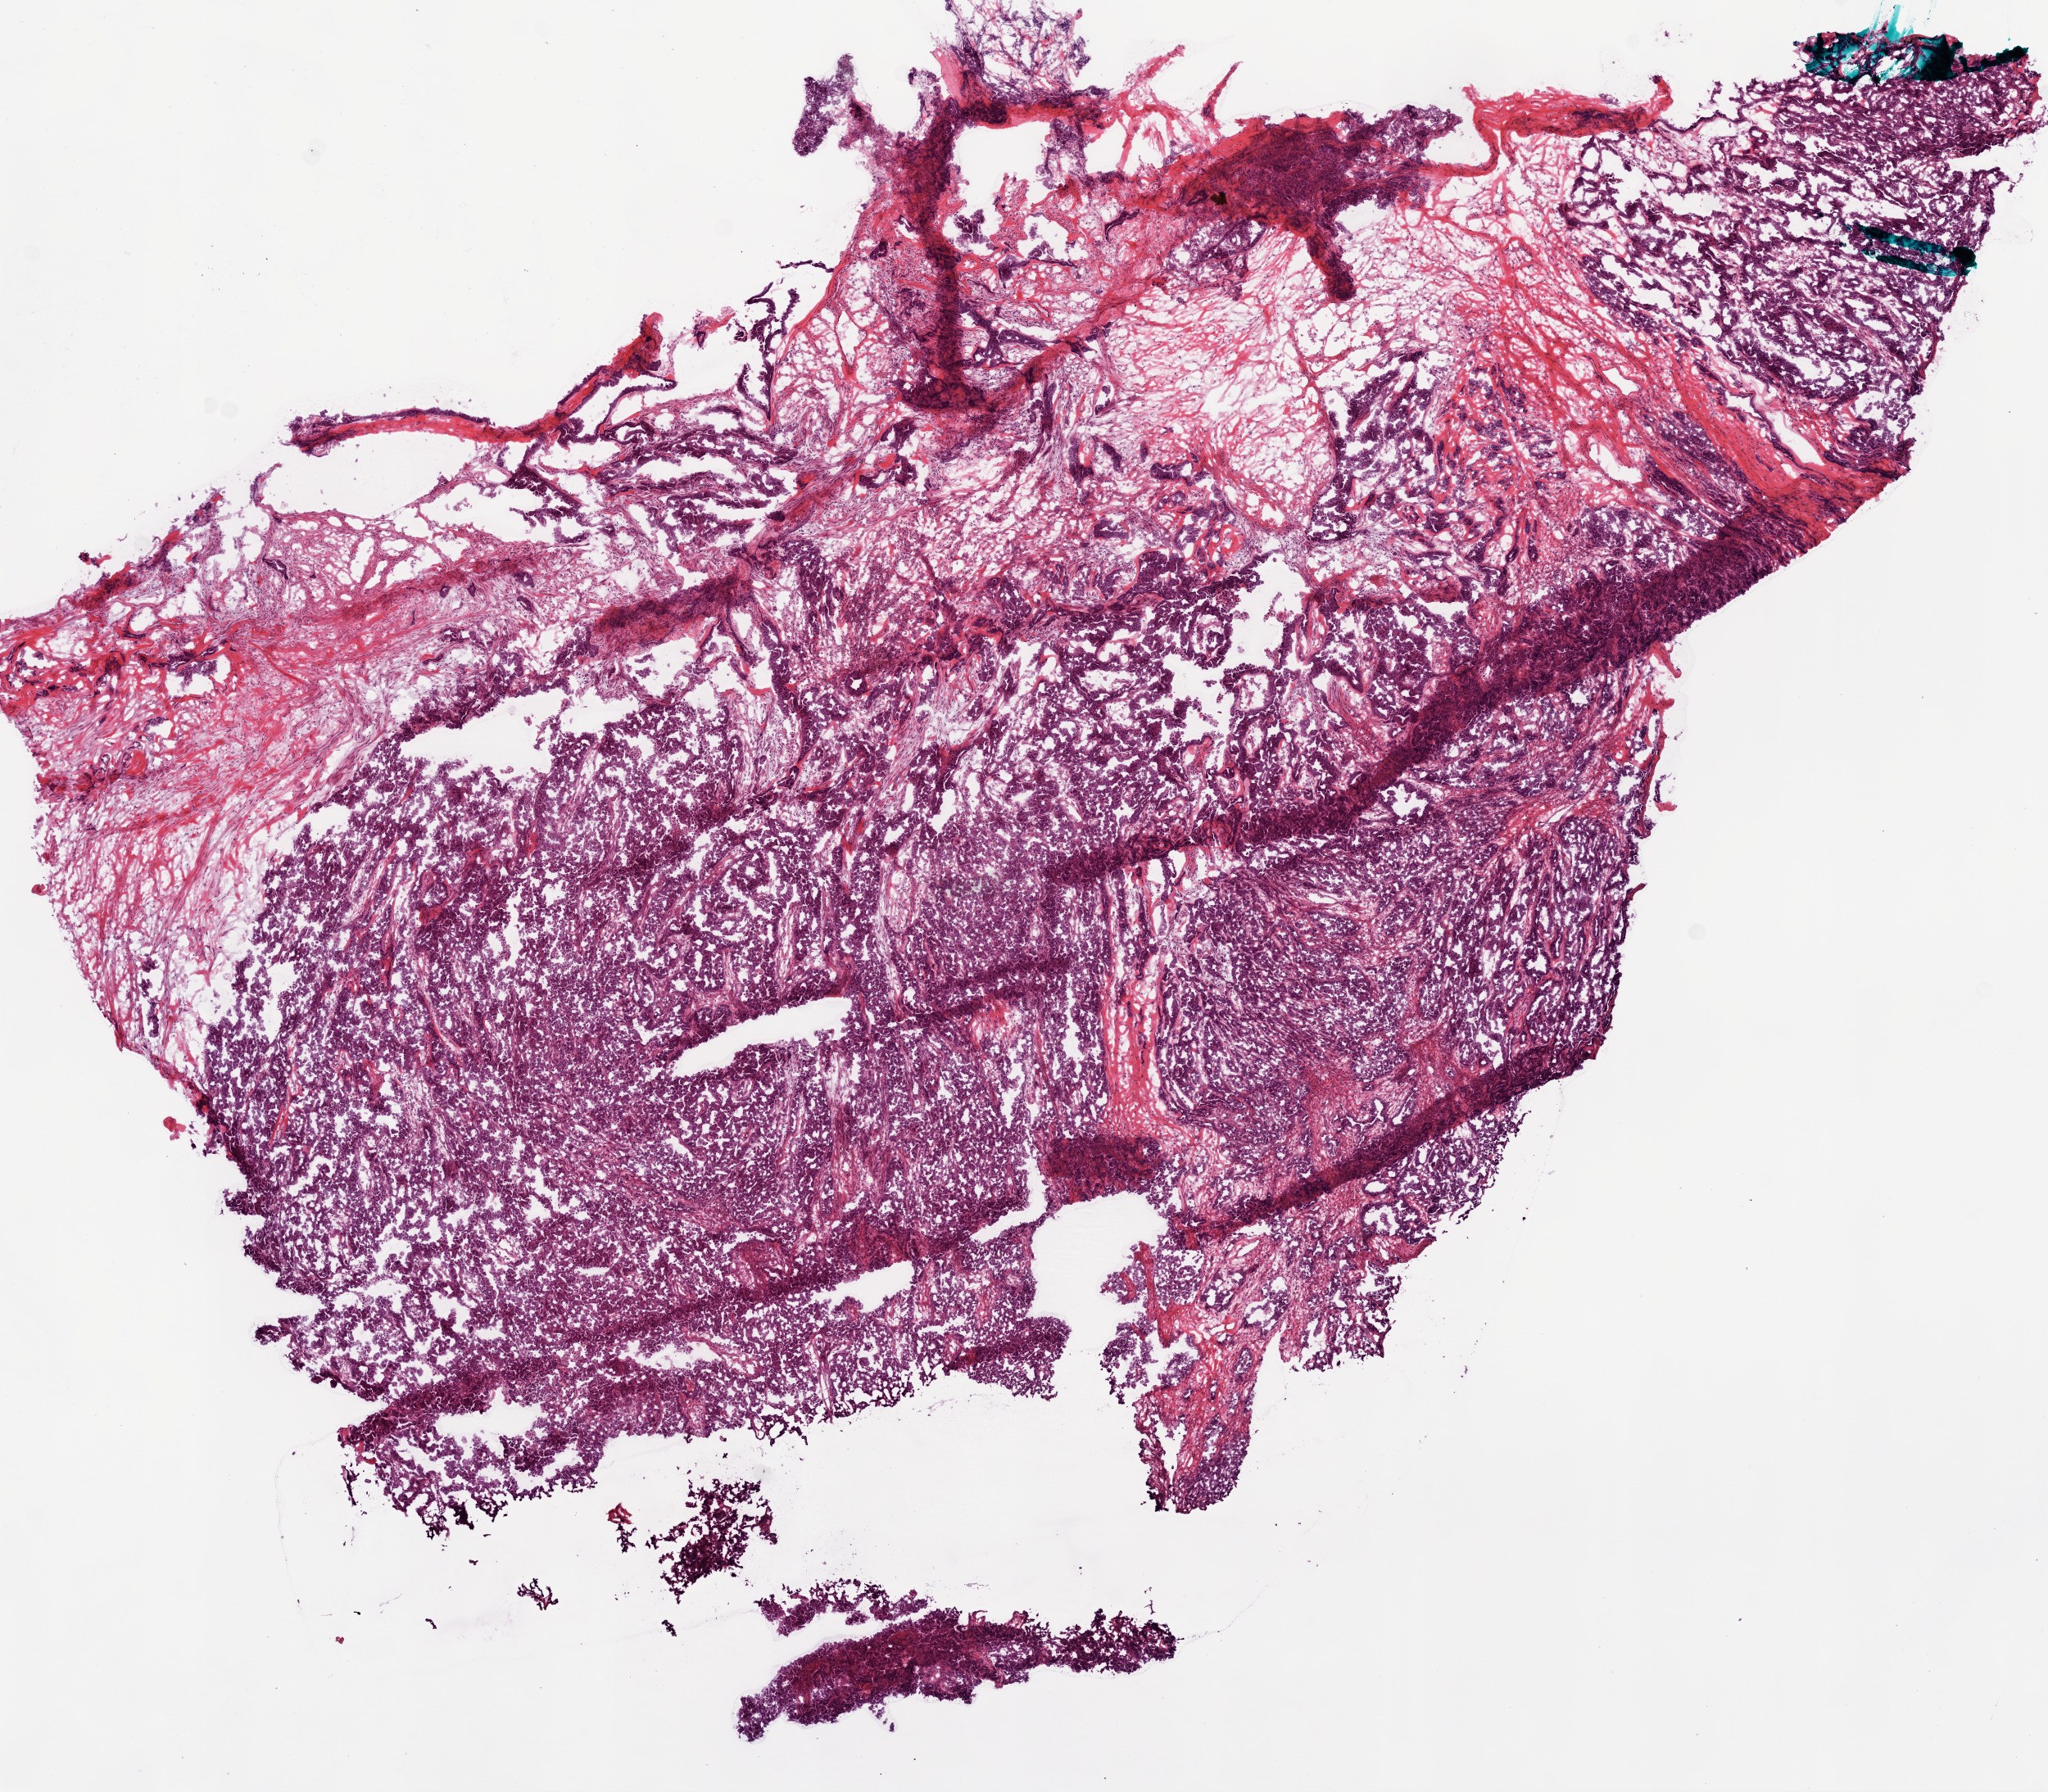
Whole-slide histology image, Hematoxylin and eosin (H&E) stained — low-resolution overview of the scanned area, about 10.0 x 8.8 mm (from a 20x scan); frozen section; ovary, primary tumour sample. Female, age 70 years at initial diagnosis. Histologic grade: G3 (poorly differentiated). Composition of this section per pathologist review: tumour cells 80%, tumour nuclei 80%, normal cells 0%, stromal cells 19%, necrosis 1%.
FIGO stage: IIIC. Diagnosis: Serous cystadenocarcinoma, NOS.